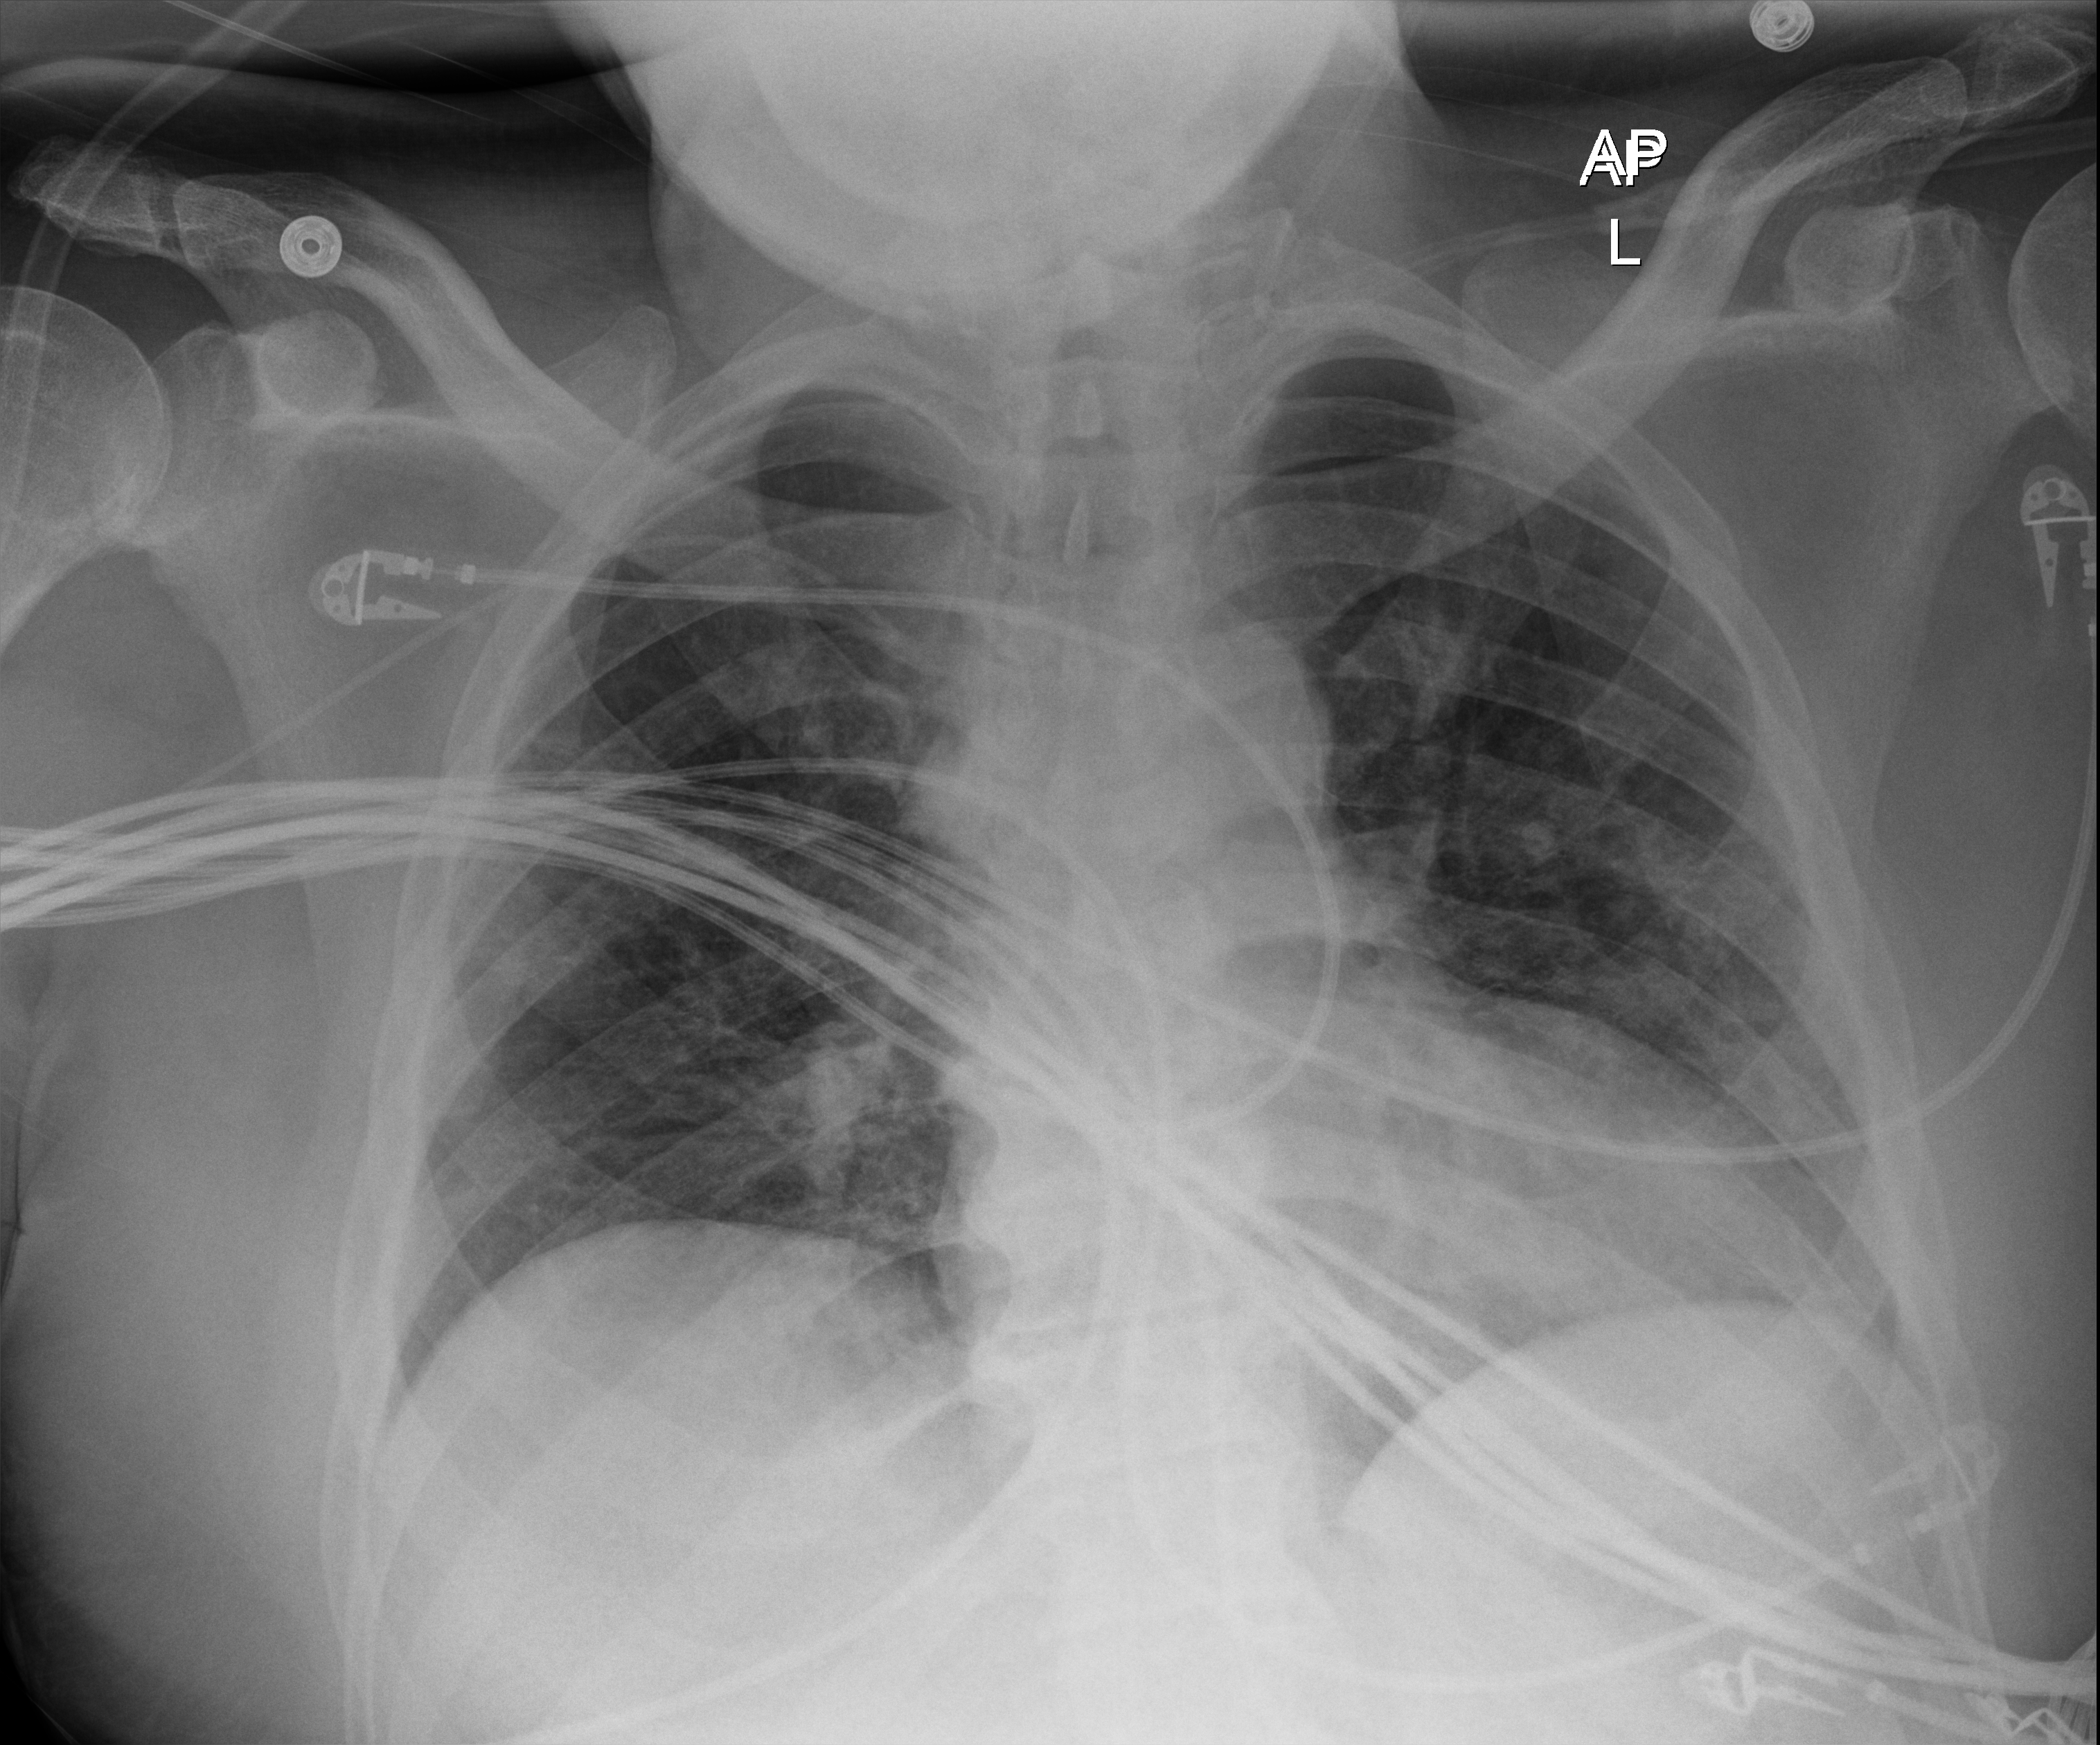
Portable chest radiograph. Male patient hospitalised with COVID-19, age 18–59 years.
Admission-level facts for this patient (not findings on this image; timing relative to this image not recorded): hypertension (admission record): no; chronic kidney disease (admission record): no.